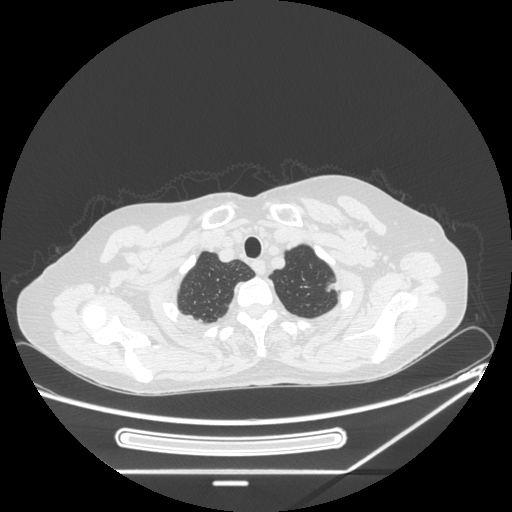
Chest CT, one axial slice. Slice 216 of 250 in the series (ordered by position). 120 kVp. Lung window (W 1500 / L -600 HU). 1.25 mm slice thickness. 512 × 512 image matrix, field of view 409 × 409 mm. Patient: female, 57 years. From the clinical record (not read from this slice): clinical TNM (as recorded): T1c N0 M0; histopathological grade: G2-3.
Outlined on this slice (bounding box drawn by a radiologist):
- lung tumour (recorded histology: adenocarcinoma): bounding box (x1, y1, x2, y2) in pixels: (322, 275, 341, 298)